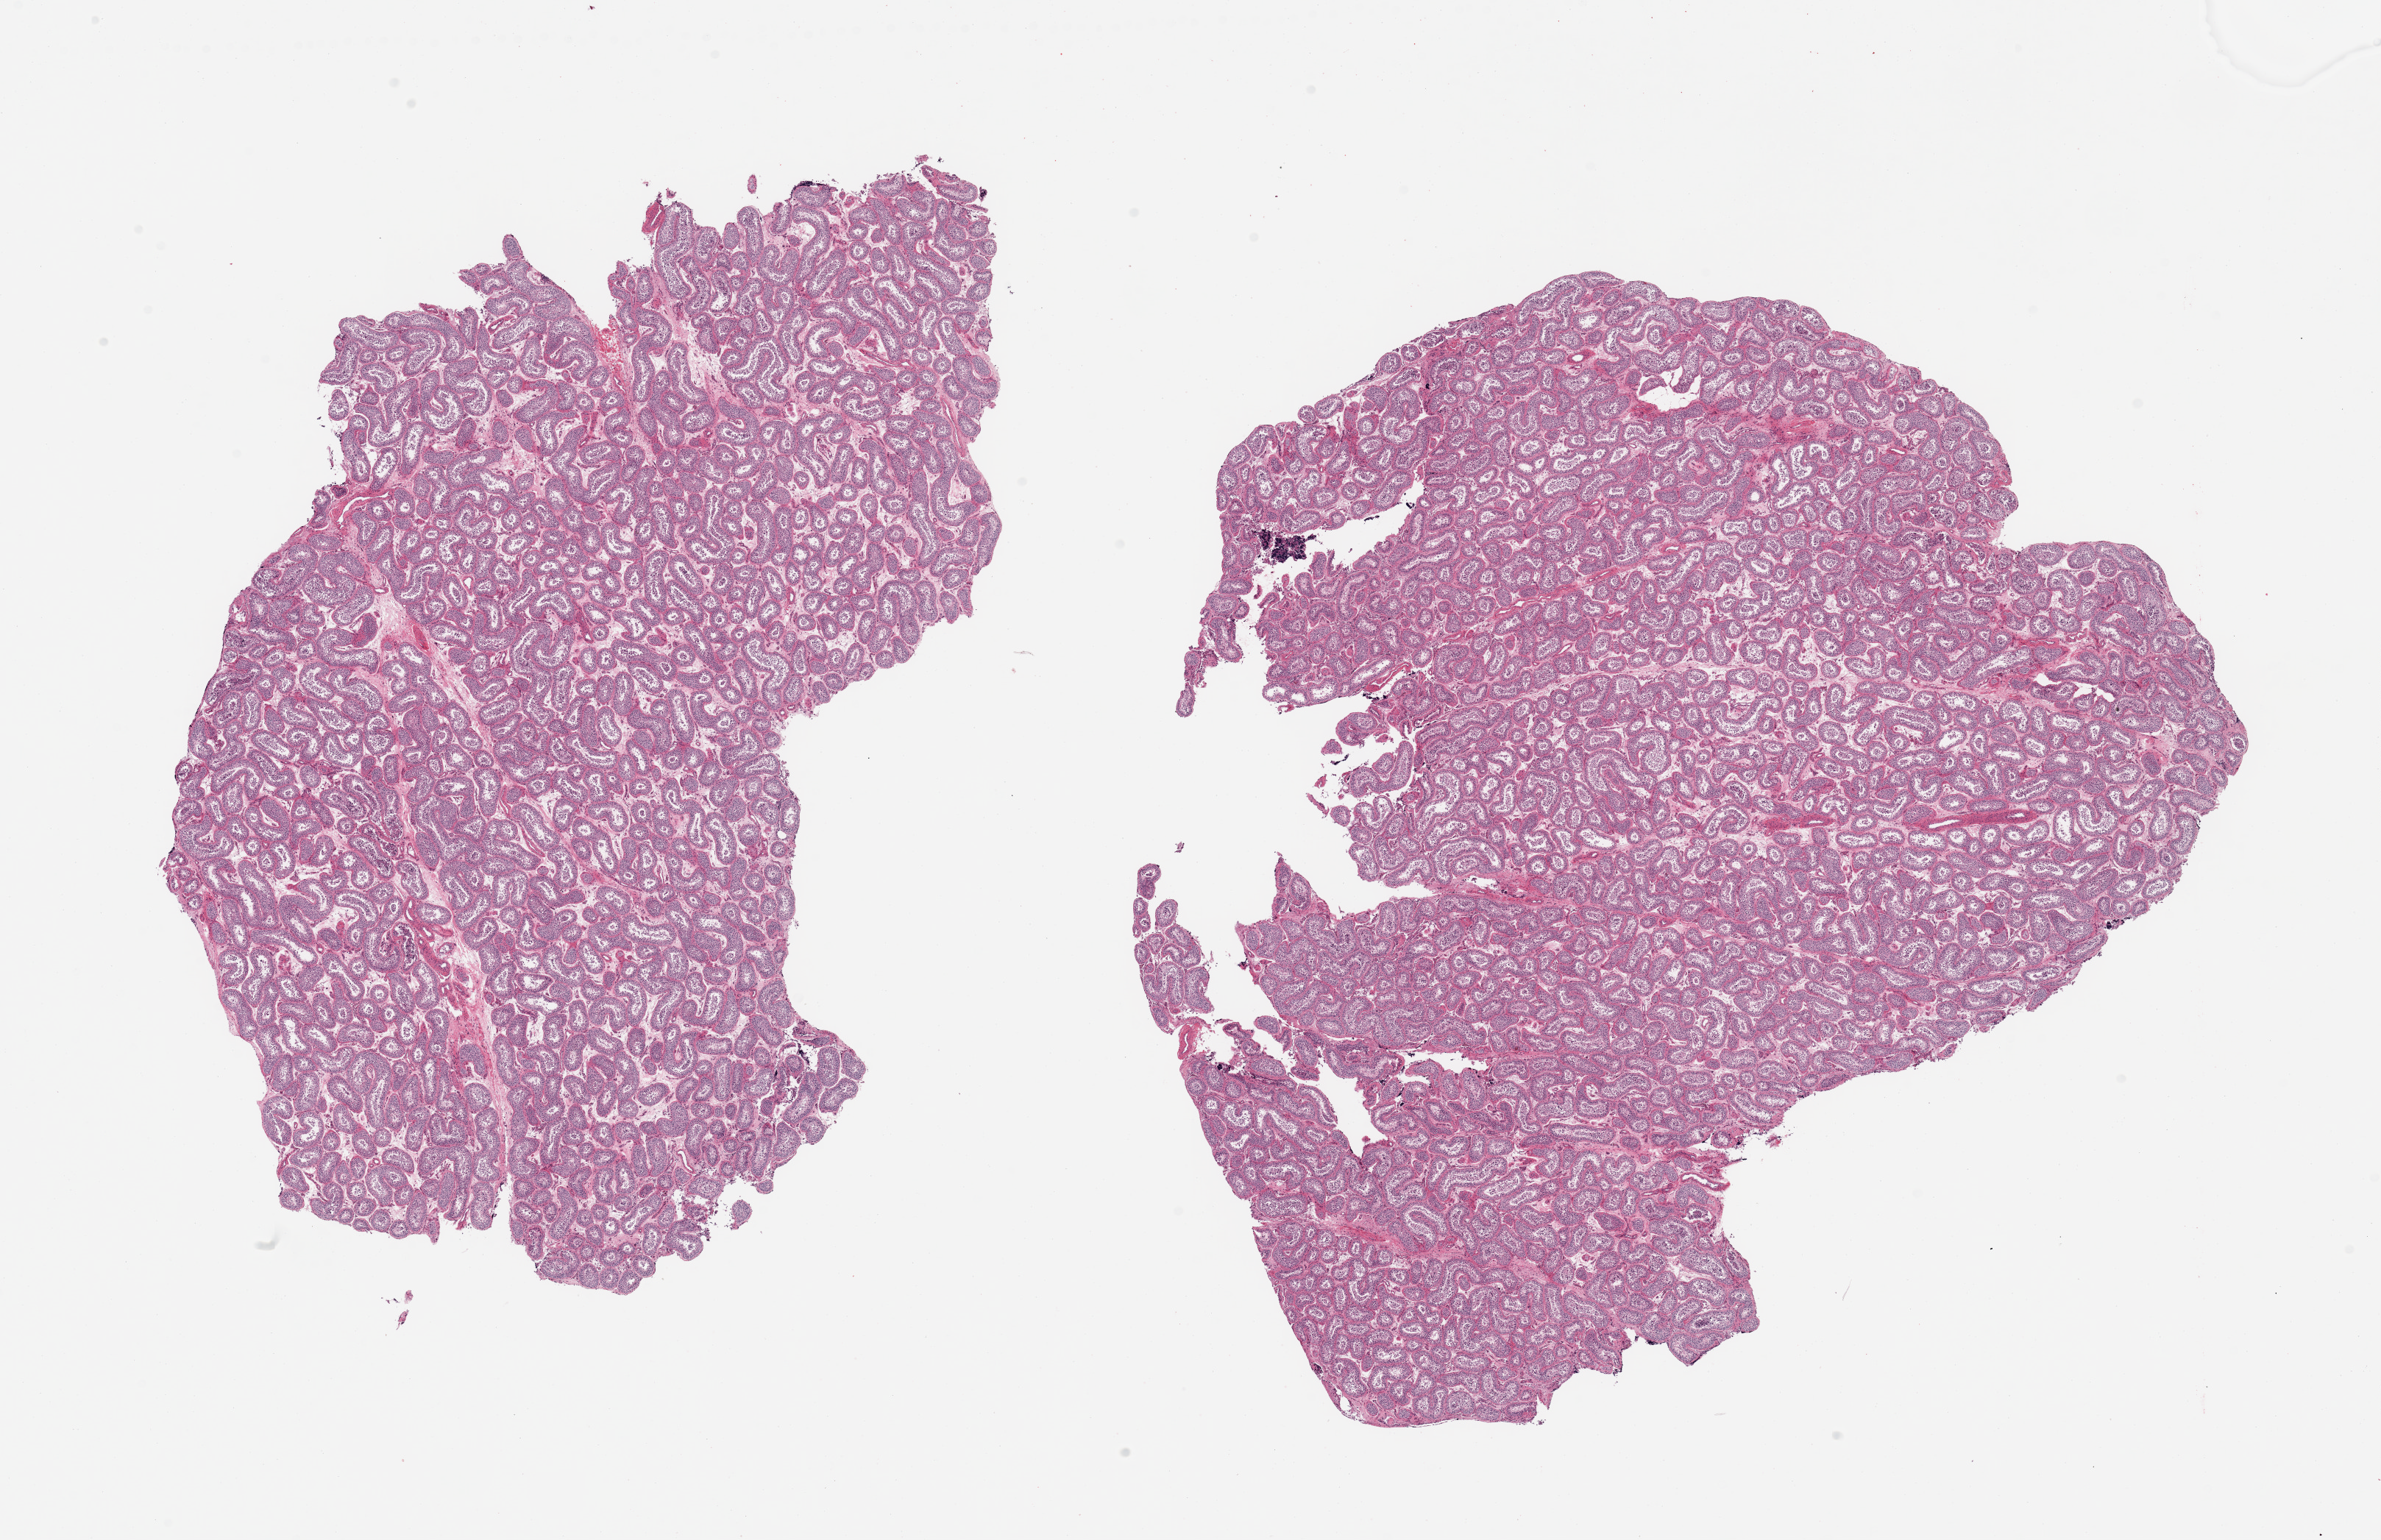
Digitized hematoxylin and eosin (H&E)-stained section, brightfield — shown as a low-resolution overview of the whole scanned area (about 25.6 x 16.6 mm, acquisition: 20x scan). PAXgene-fixed, paraffin-embedded tissue. Section of testis (target tissue). Tissue donor sample. Donor: male.
Reviewer comment on this tissue sample: 2 pieces; spermatogenesis.